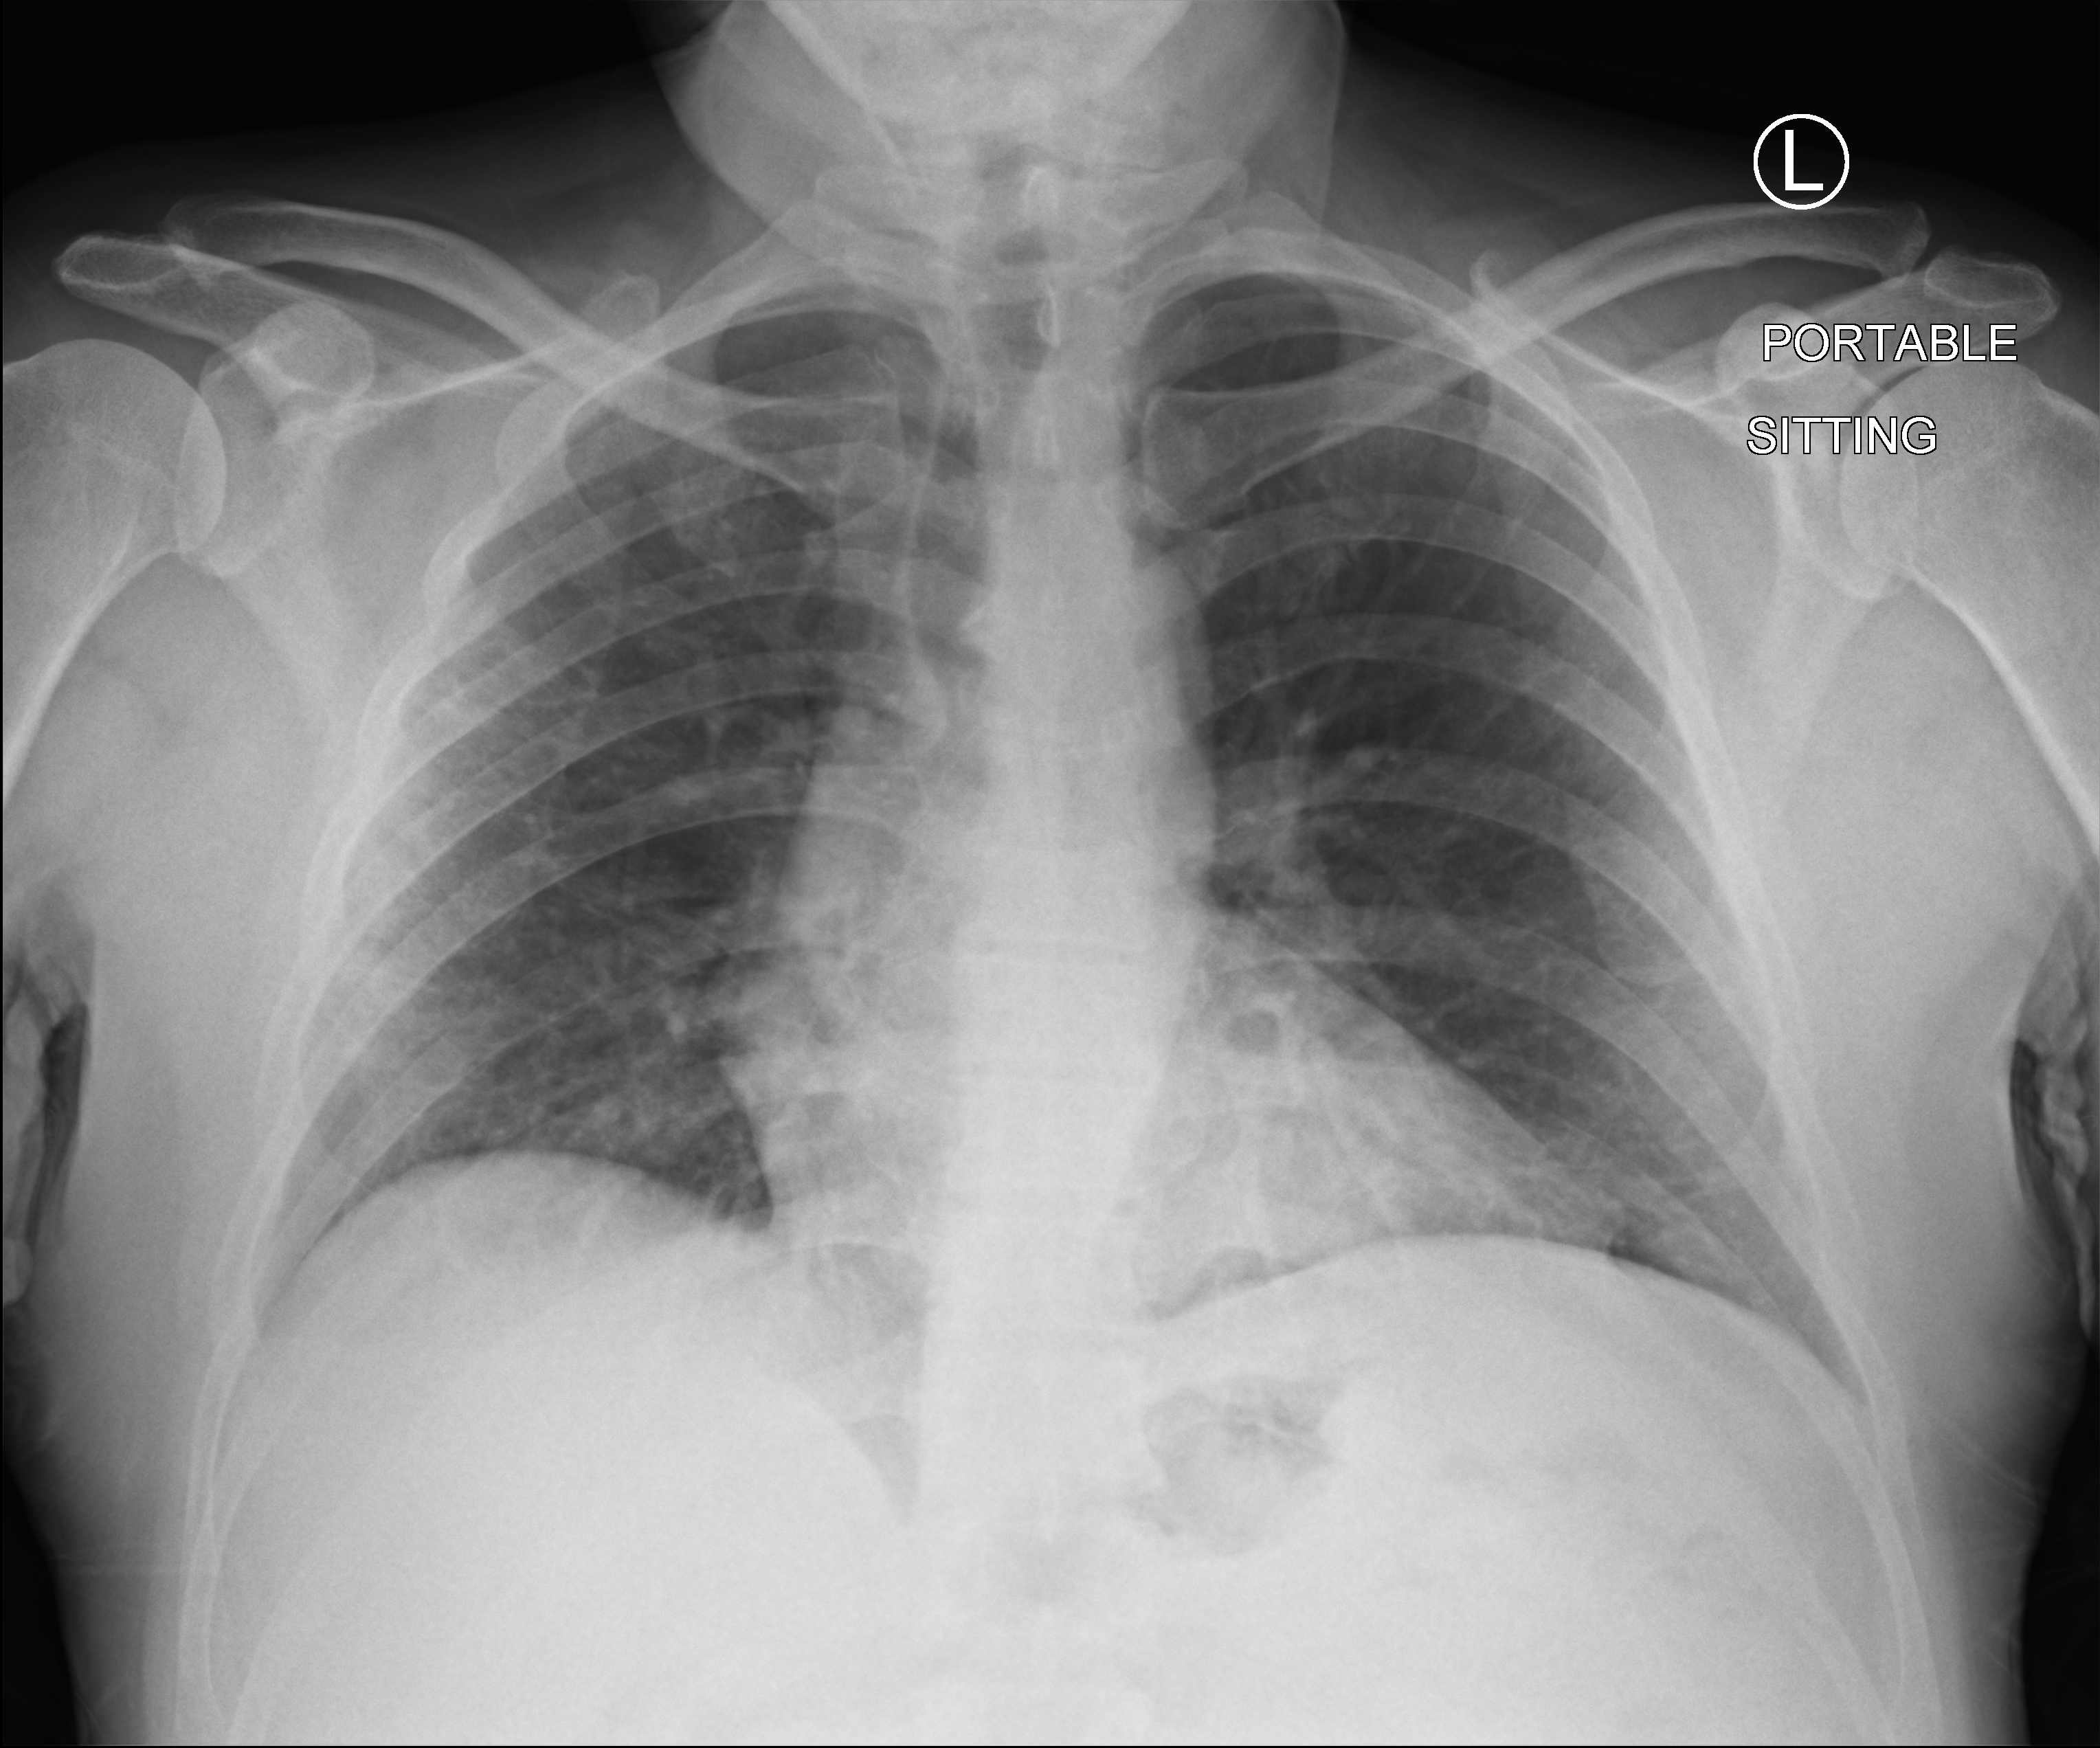
Chest X-ray (portable). Male patient hospitalised with COVID-19, age 18–59 years.
Admission-level facts for this patient (not findings on this image; timing relative to this image not recorded):
- admitted to intensive care during this hospital stay: no
- mechanically ventilated during this hospital stay: no
- COPD (admission record): no